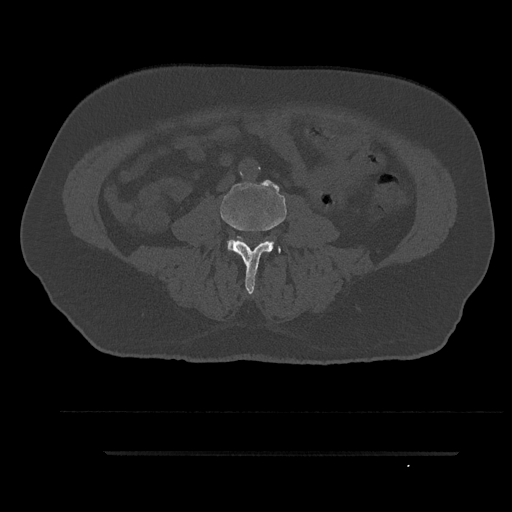
CT including the spine, one axial slice. Reconstruction kernel Br40s/3. Bone window (W 1800 / L 400 HU). 0.5 mm slice thickness. 512 × 512 image matrix, field of view 432 × 432 mm. Male patient, age 63 years. From the clinical record (not read from this slice): primary cancer: renal; vertebrae with lytic lesions (as recorded): T8.
Structures marked on this image (semi-automatic segmentation, software-assisted and operator-edited):
- L3 vertebra: bounding box <221,185,286,295> (left, top, right, bottom; pixels)
- L4 vertebra: <269,241,281,254>